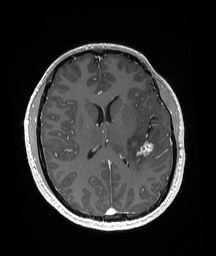
Brain MRI from a brain-tumour surgery series, one axial slice; position 79 of 192 along the scan axis; T1-weighted post-contrast; 1 mm slice thickness; 216 × 256 image matrix, field of view 211 × 250 mm. Case-level facts recorded for this patient, not image findings: histopathology: Glioneuronal tumor; WHO grade: 2; tumour location: Left Superior Temporal Gyrus.
Outlined on this slice (expert manual segmentation):
- tumour: bounding box (x1, y1, x2, y2) in pixels: (139, 140, 155, 157)